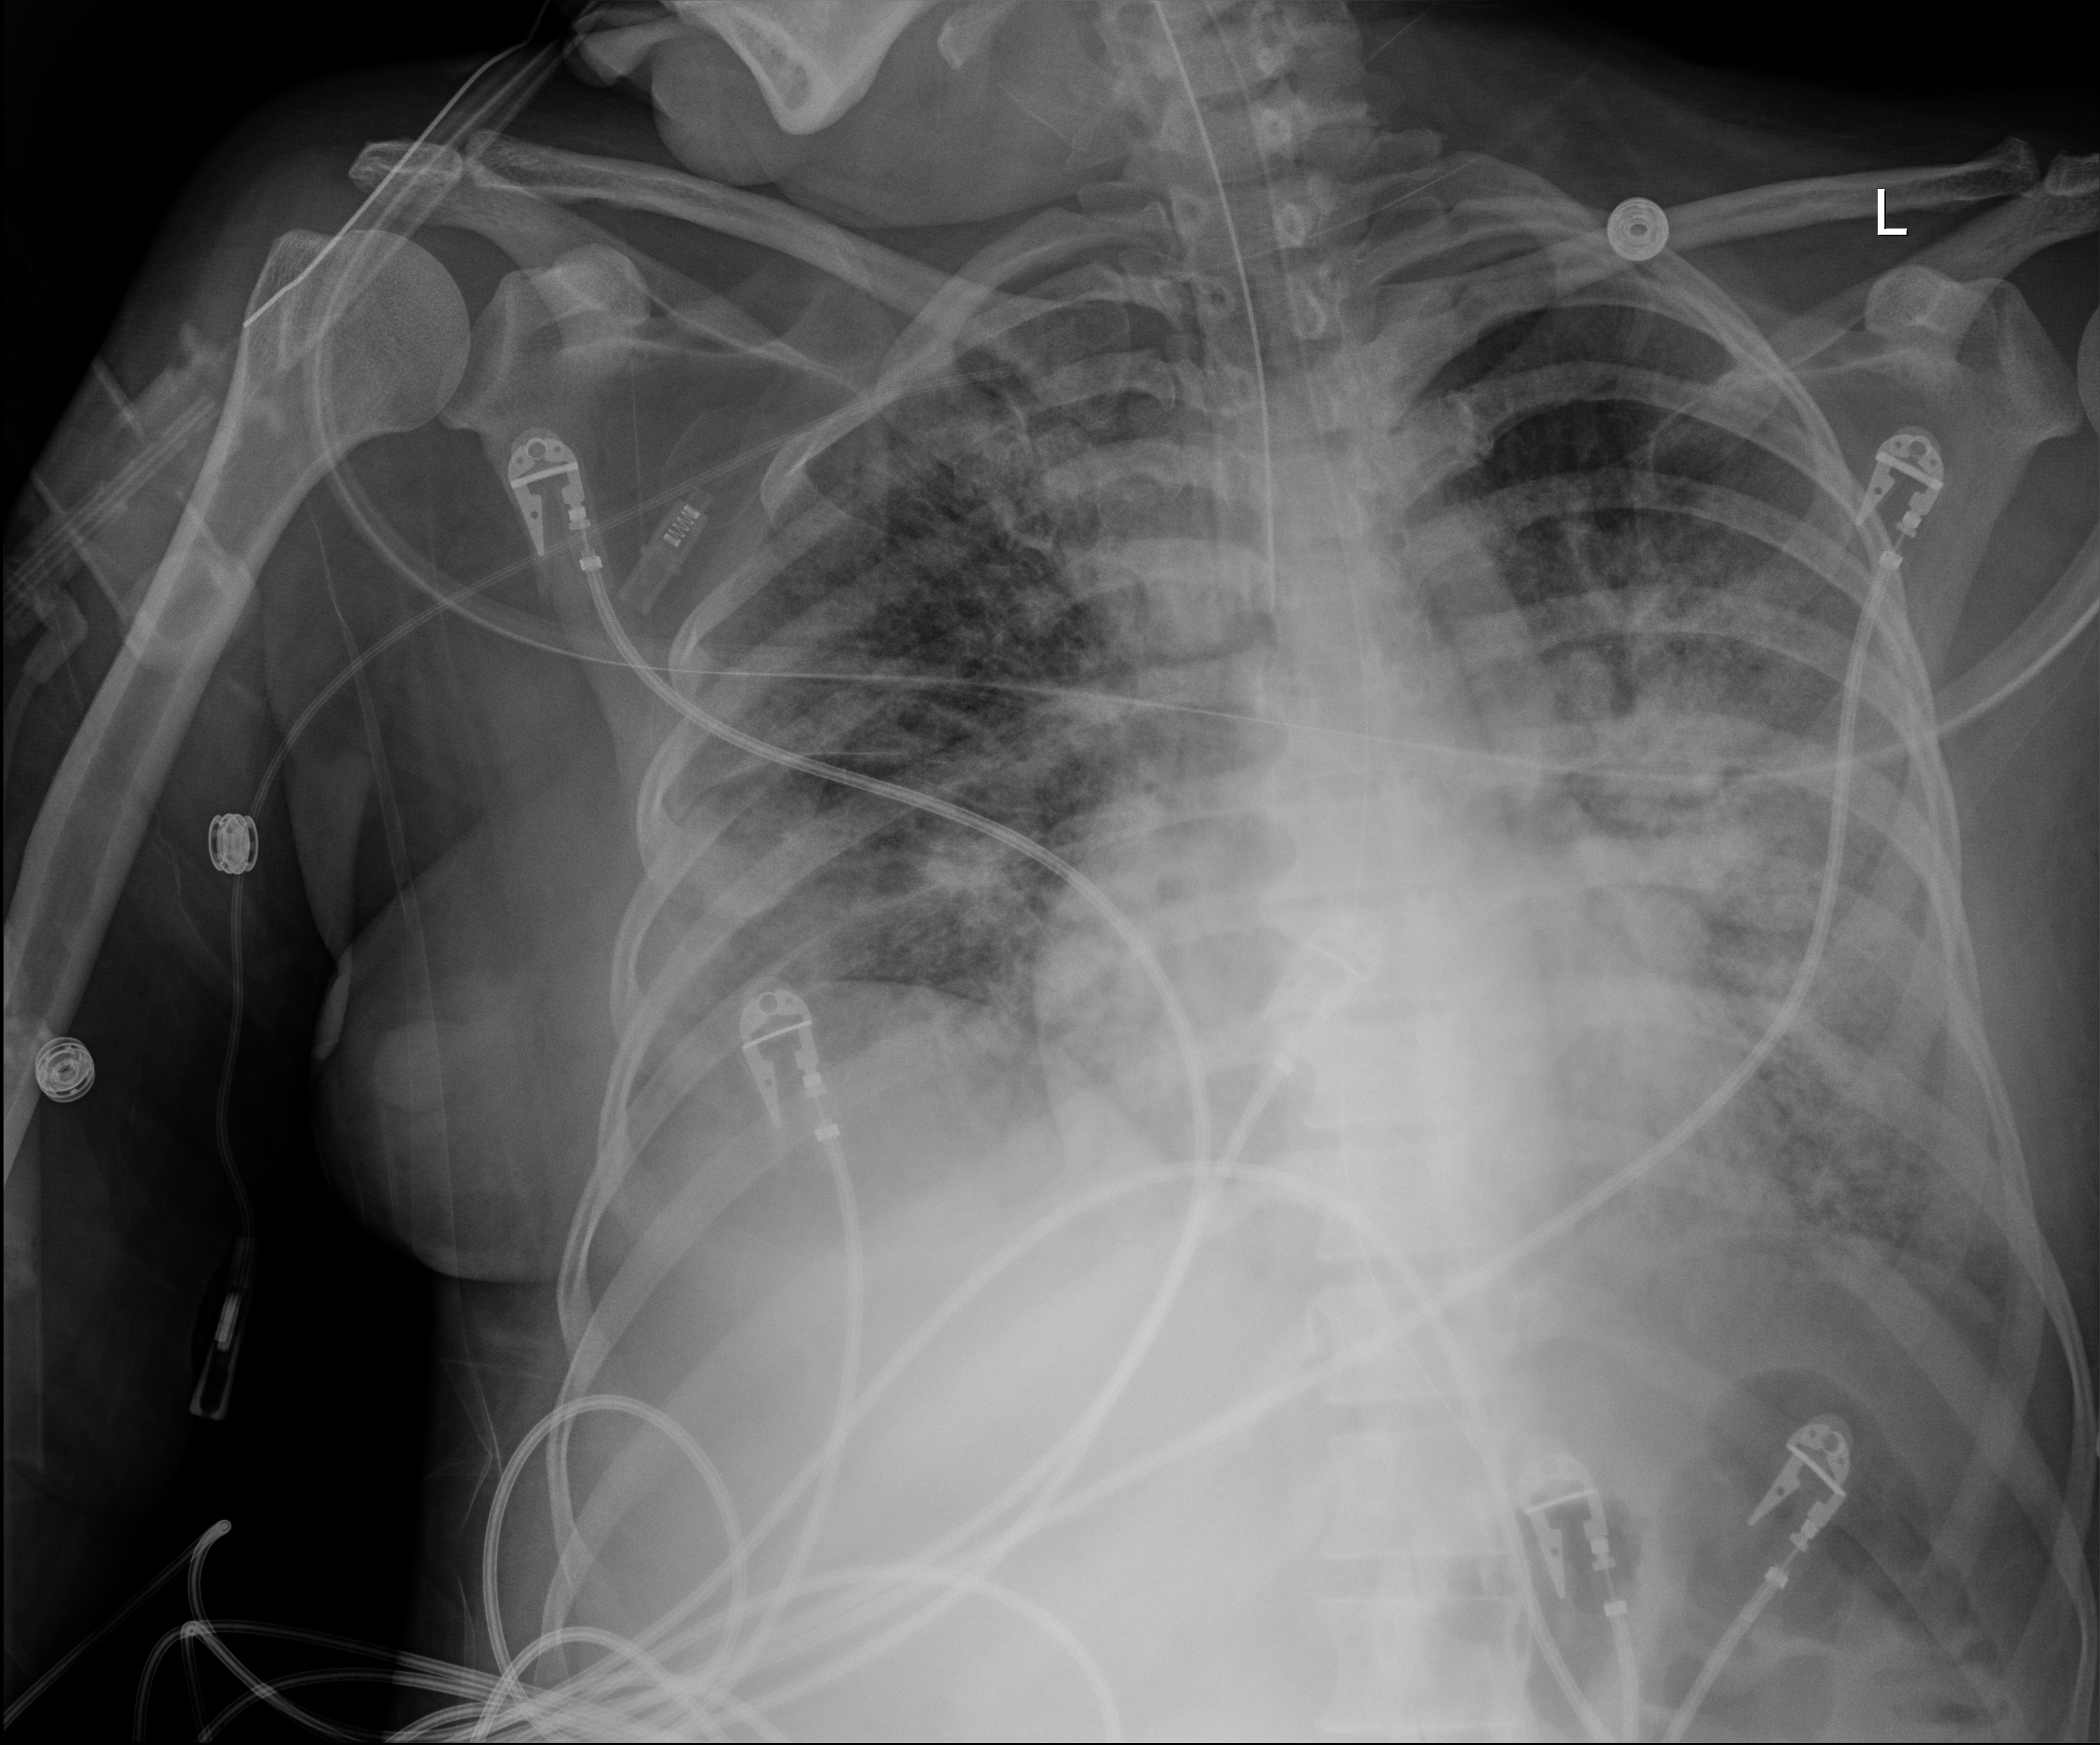
Chest X-ray (portable); anteroposterior (AP) projection. Female patient hospitalised with COVID-19, age 18–59 years.
From the hospital-stay record, not from the radiograph (when in the stay this image was taken is not recorded): length of hospital stay: 71 days; admitted to intensive care during this hospital stay: yes.